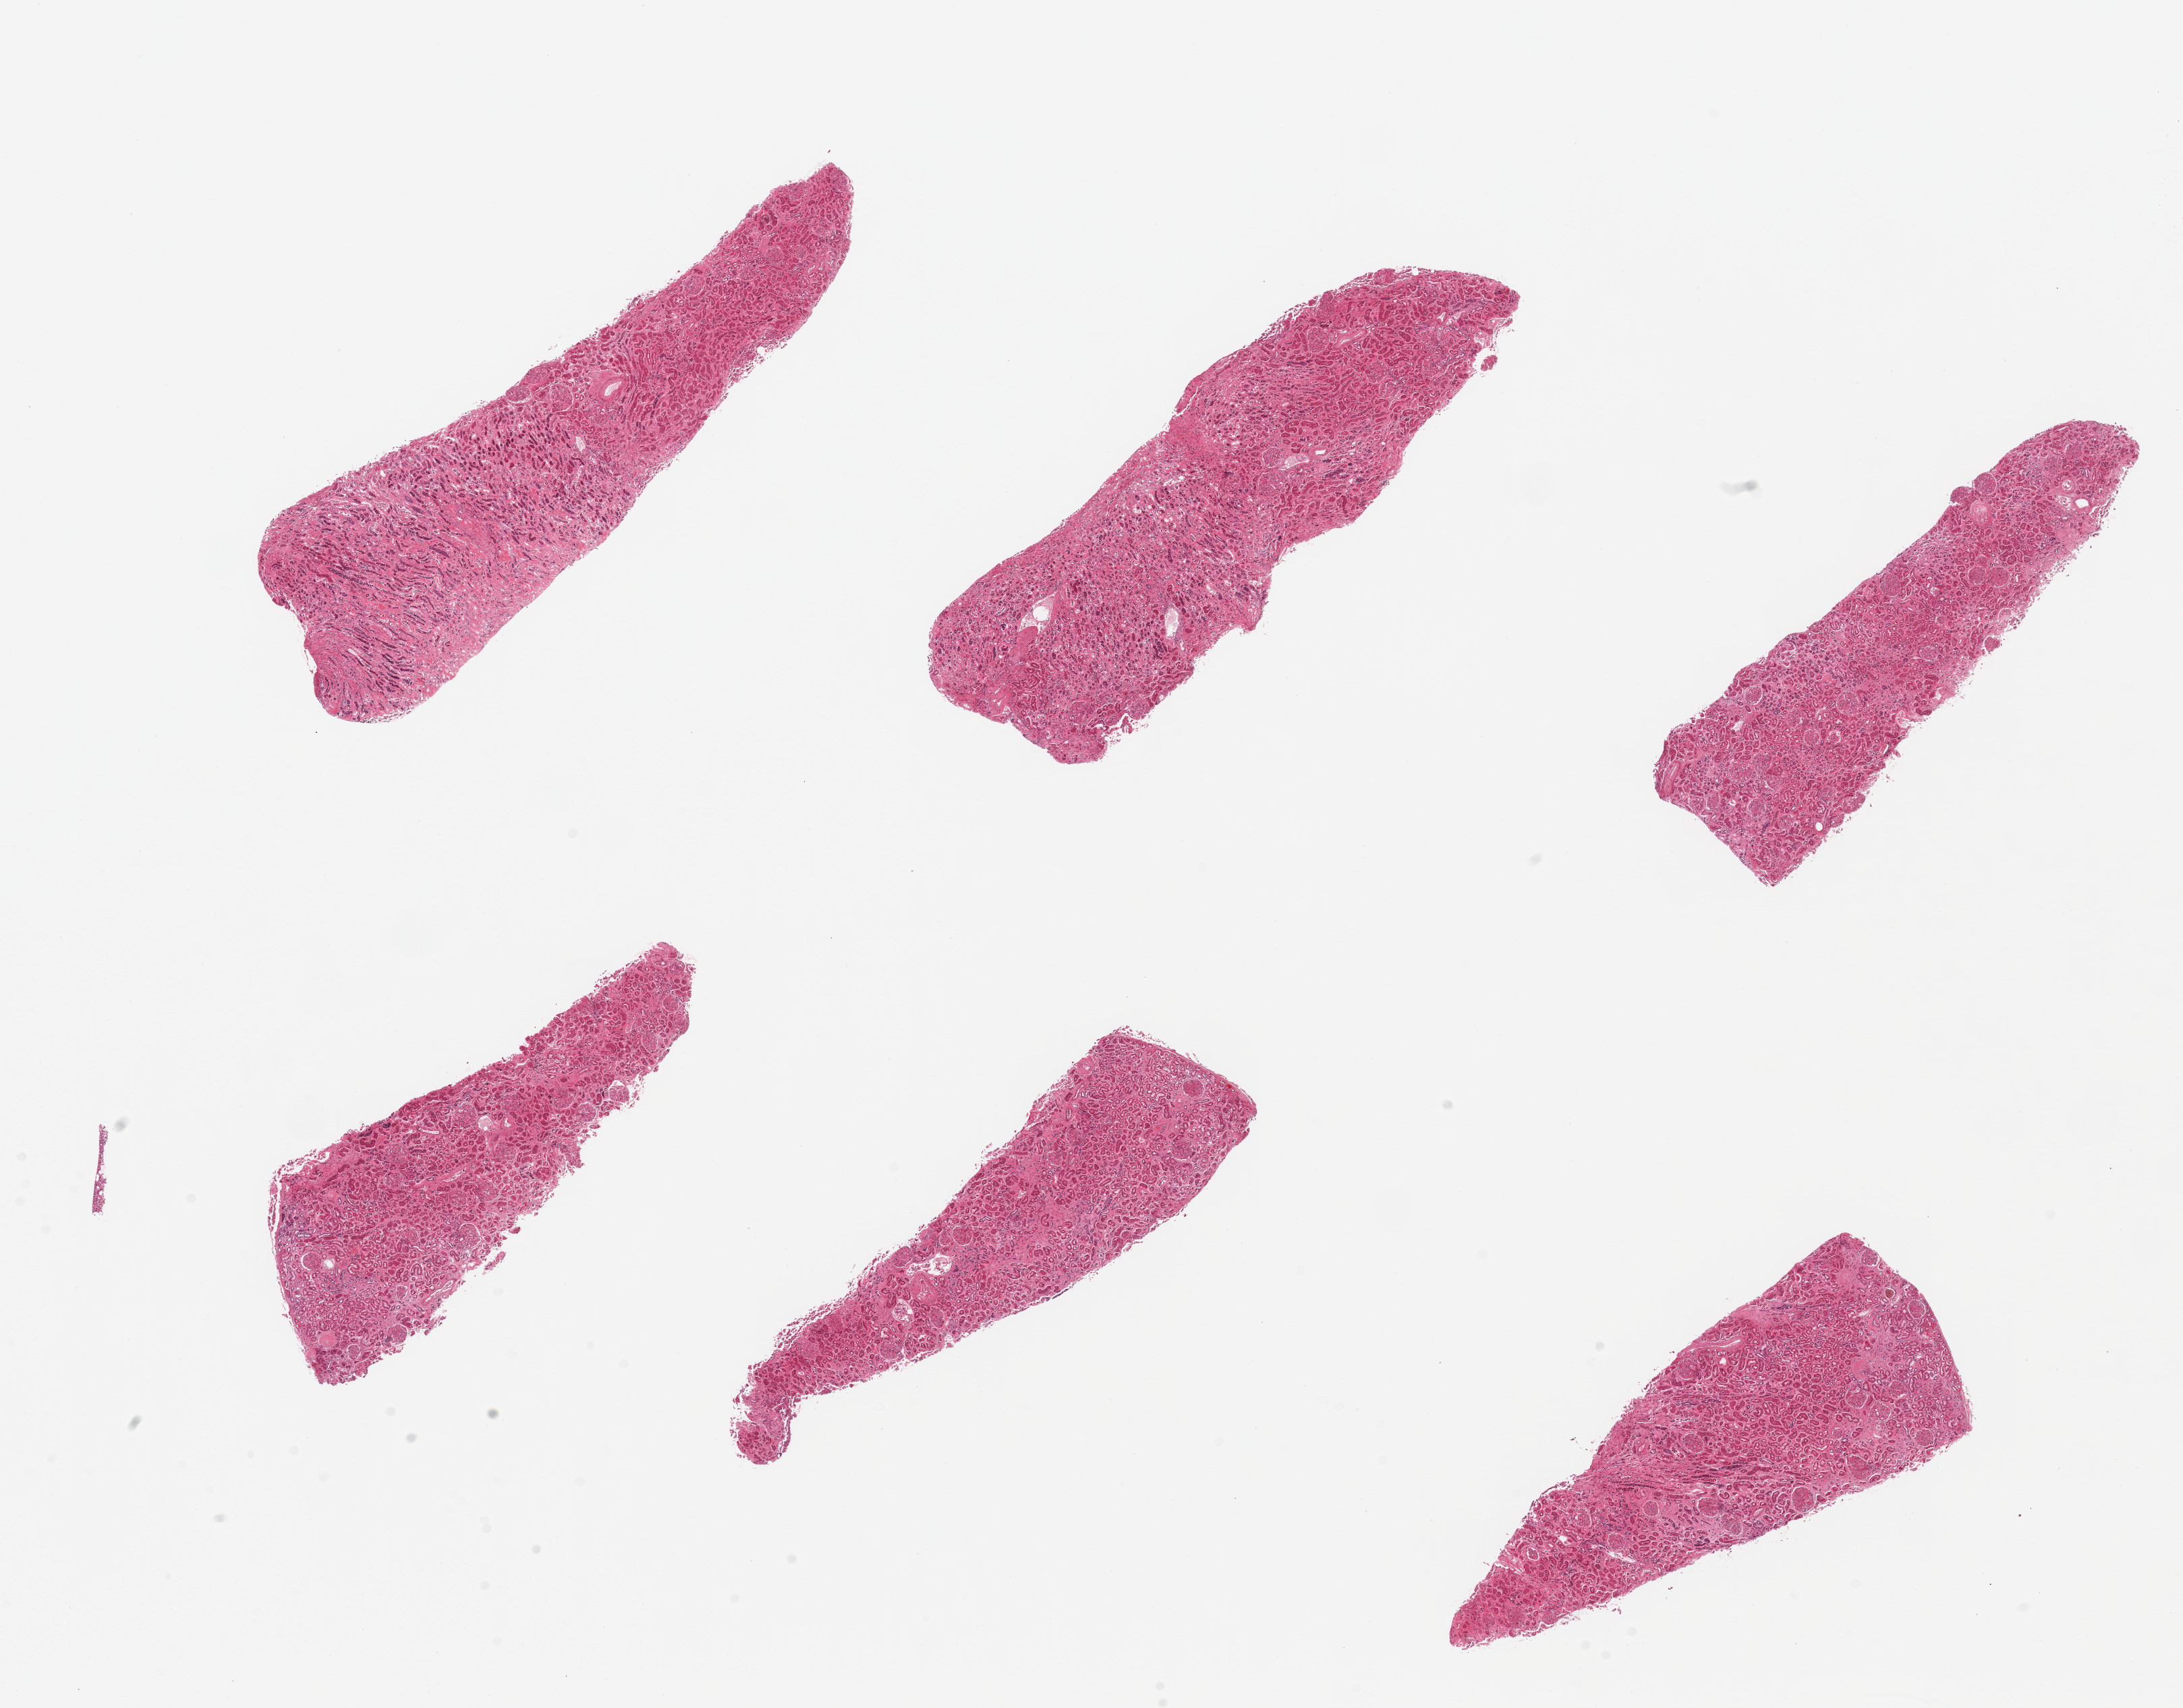
H&E whole-slide image, brightfield, shown as a low-resolution overview of the whole scanned area (about 25.6 x 20.0 mm), PAXgene-fixed paraffin-embedded (PFPE) section, section of renal cortex (target tissue), donor tissue sample. Male donor.
Pathologist's review note for this sample: 6 pieces; glomeruli in all sections, small portion of medulla also present, few sclerotic glomeruli, interstitial fibrosis and vascular thickening.